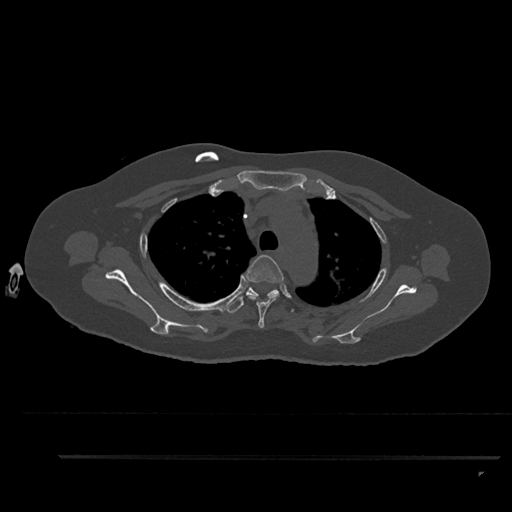
CT including the spine, one axial slice; position 666 of 797 along the scan axis; reconstruction kernel Br40s/3; 120 kVp; bone window (W 1800 / L 400 HU); 0.5 mm slice thickness; 512 × 512 image matrix, field of view 408 × 408 mm. Patient: female, 44 years. From the clinical record (not read from this slice): primary cancer: renal; vertebrae with lytic lesions (as recorded): L1.
Outlined on this slice (semi-automatically segmented with operator editing):
- T3 vertebra: bounding box [x1, y1, x2, y2] px = [243, 255, 284, 328]
- T4 vertebra: [227, 287, 294, 313]